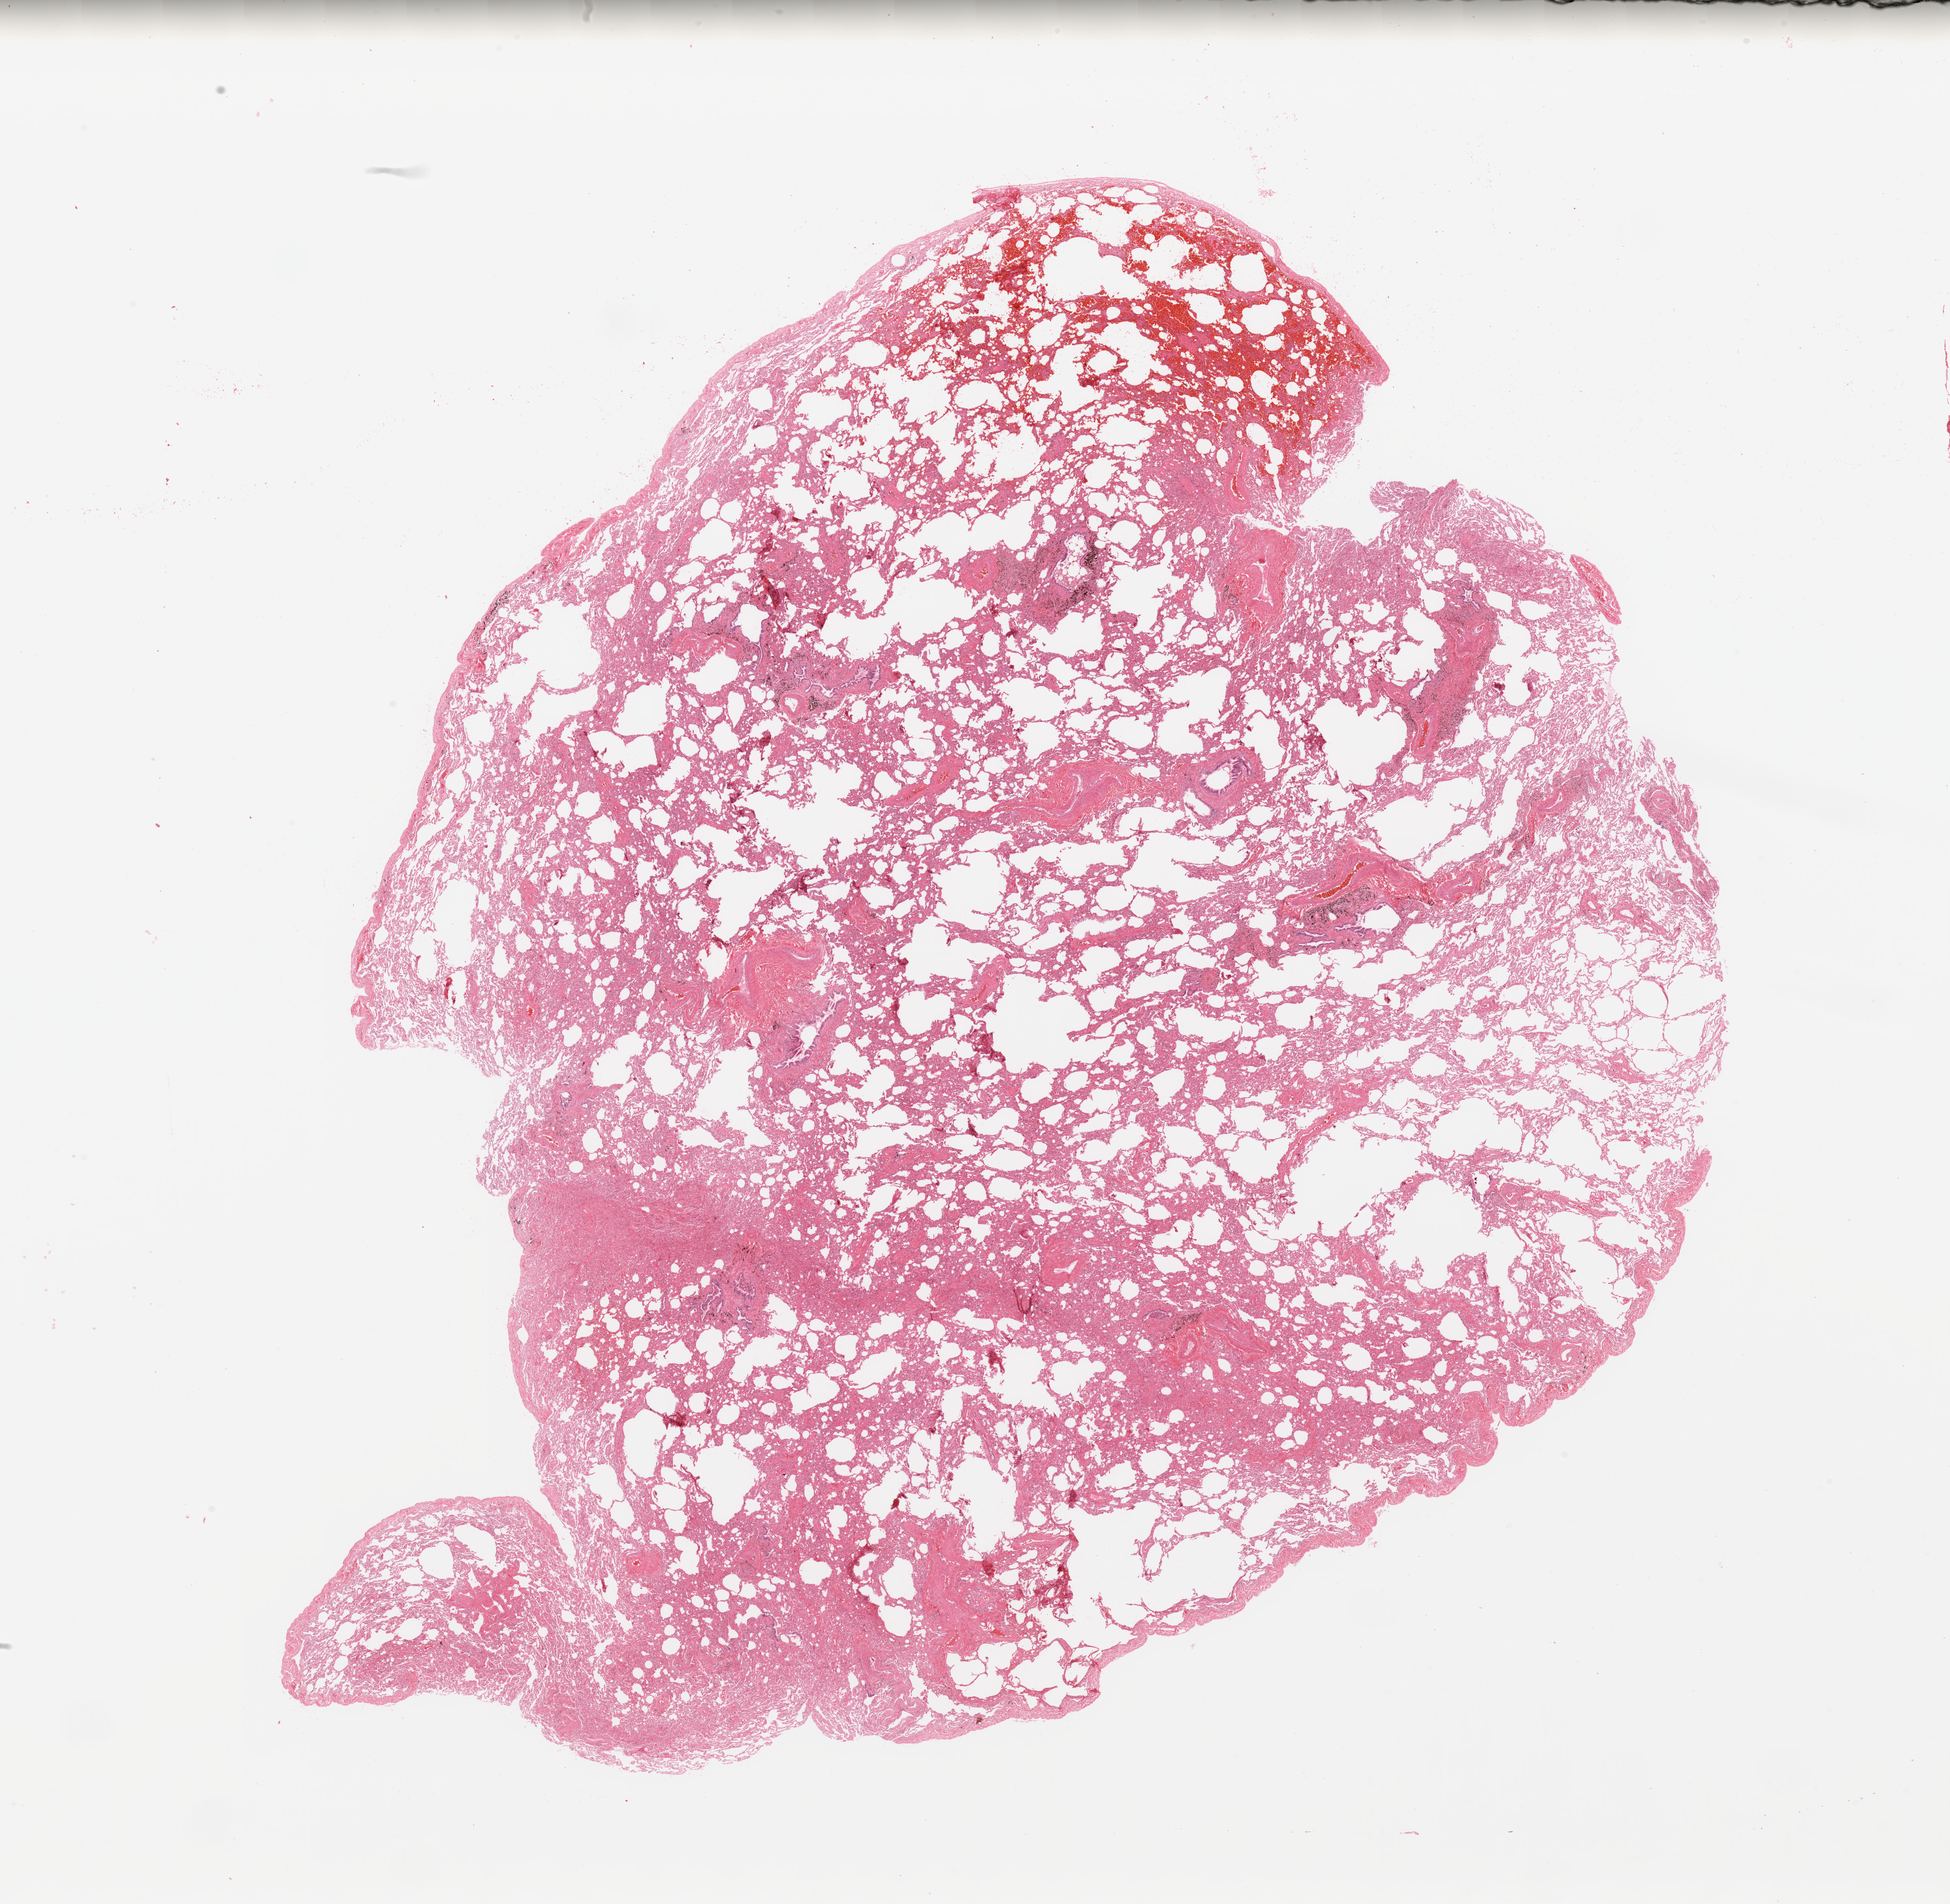
Digitized H&E tissue section (whole slide), whole scanned area (about 23.6 x 23.1 mm, acquisition: 20x scan) shown as a low-resolution overview; normal (non-tumour) tissue sample, sampled site: lung. 69-year-old female patient.
- this section: normal (non-tumour) tissue from the same patient
- patient diagnosis: Adenocarcinoma, NOS